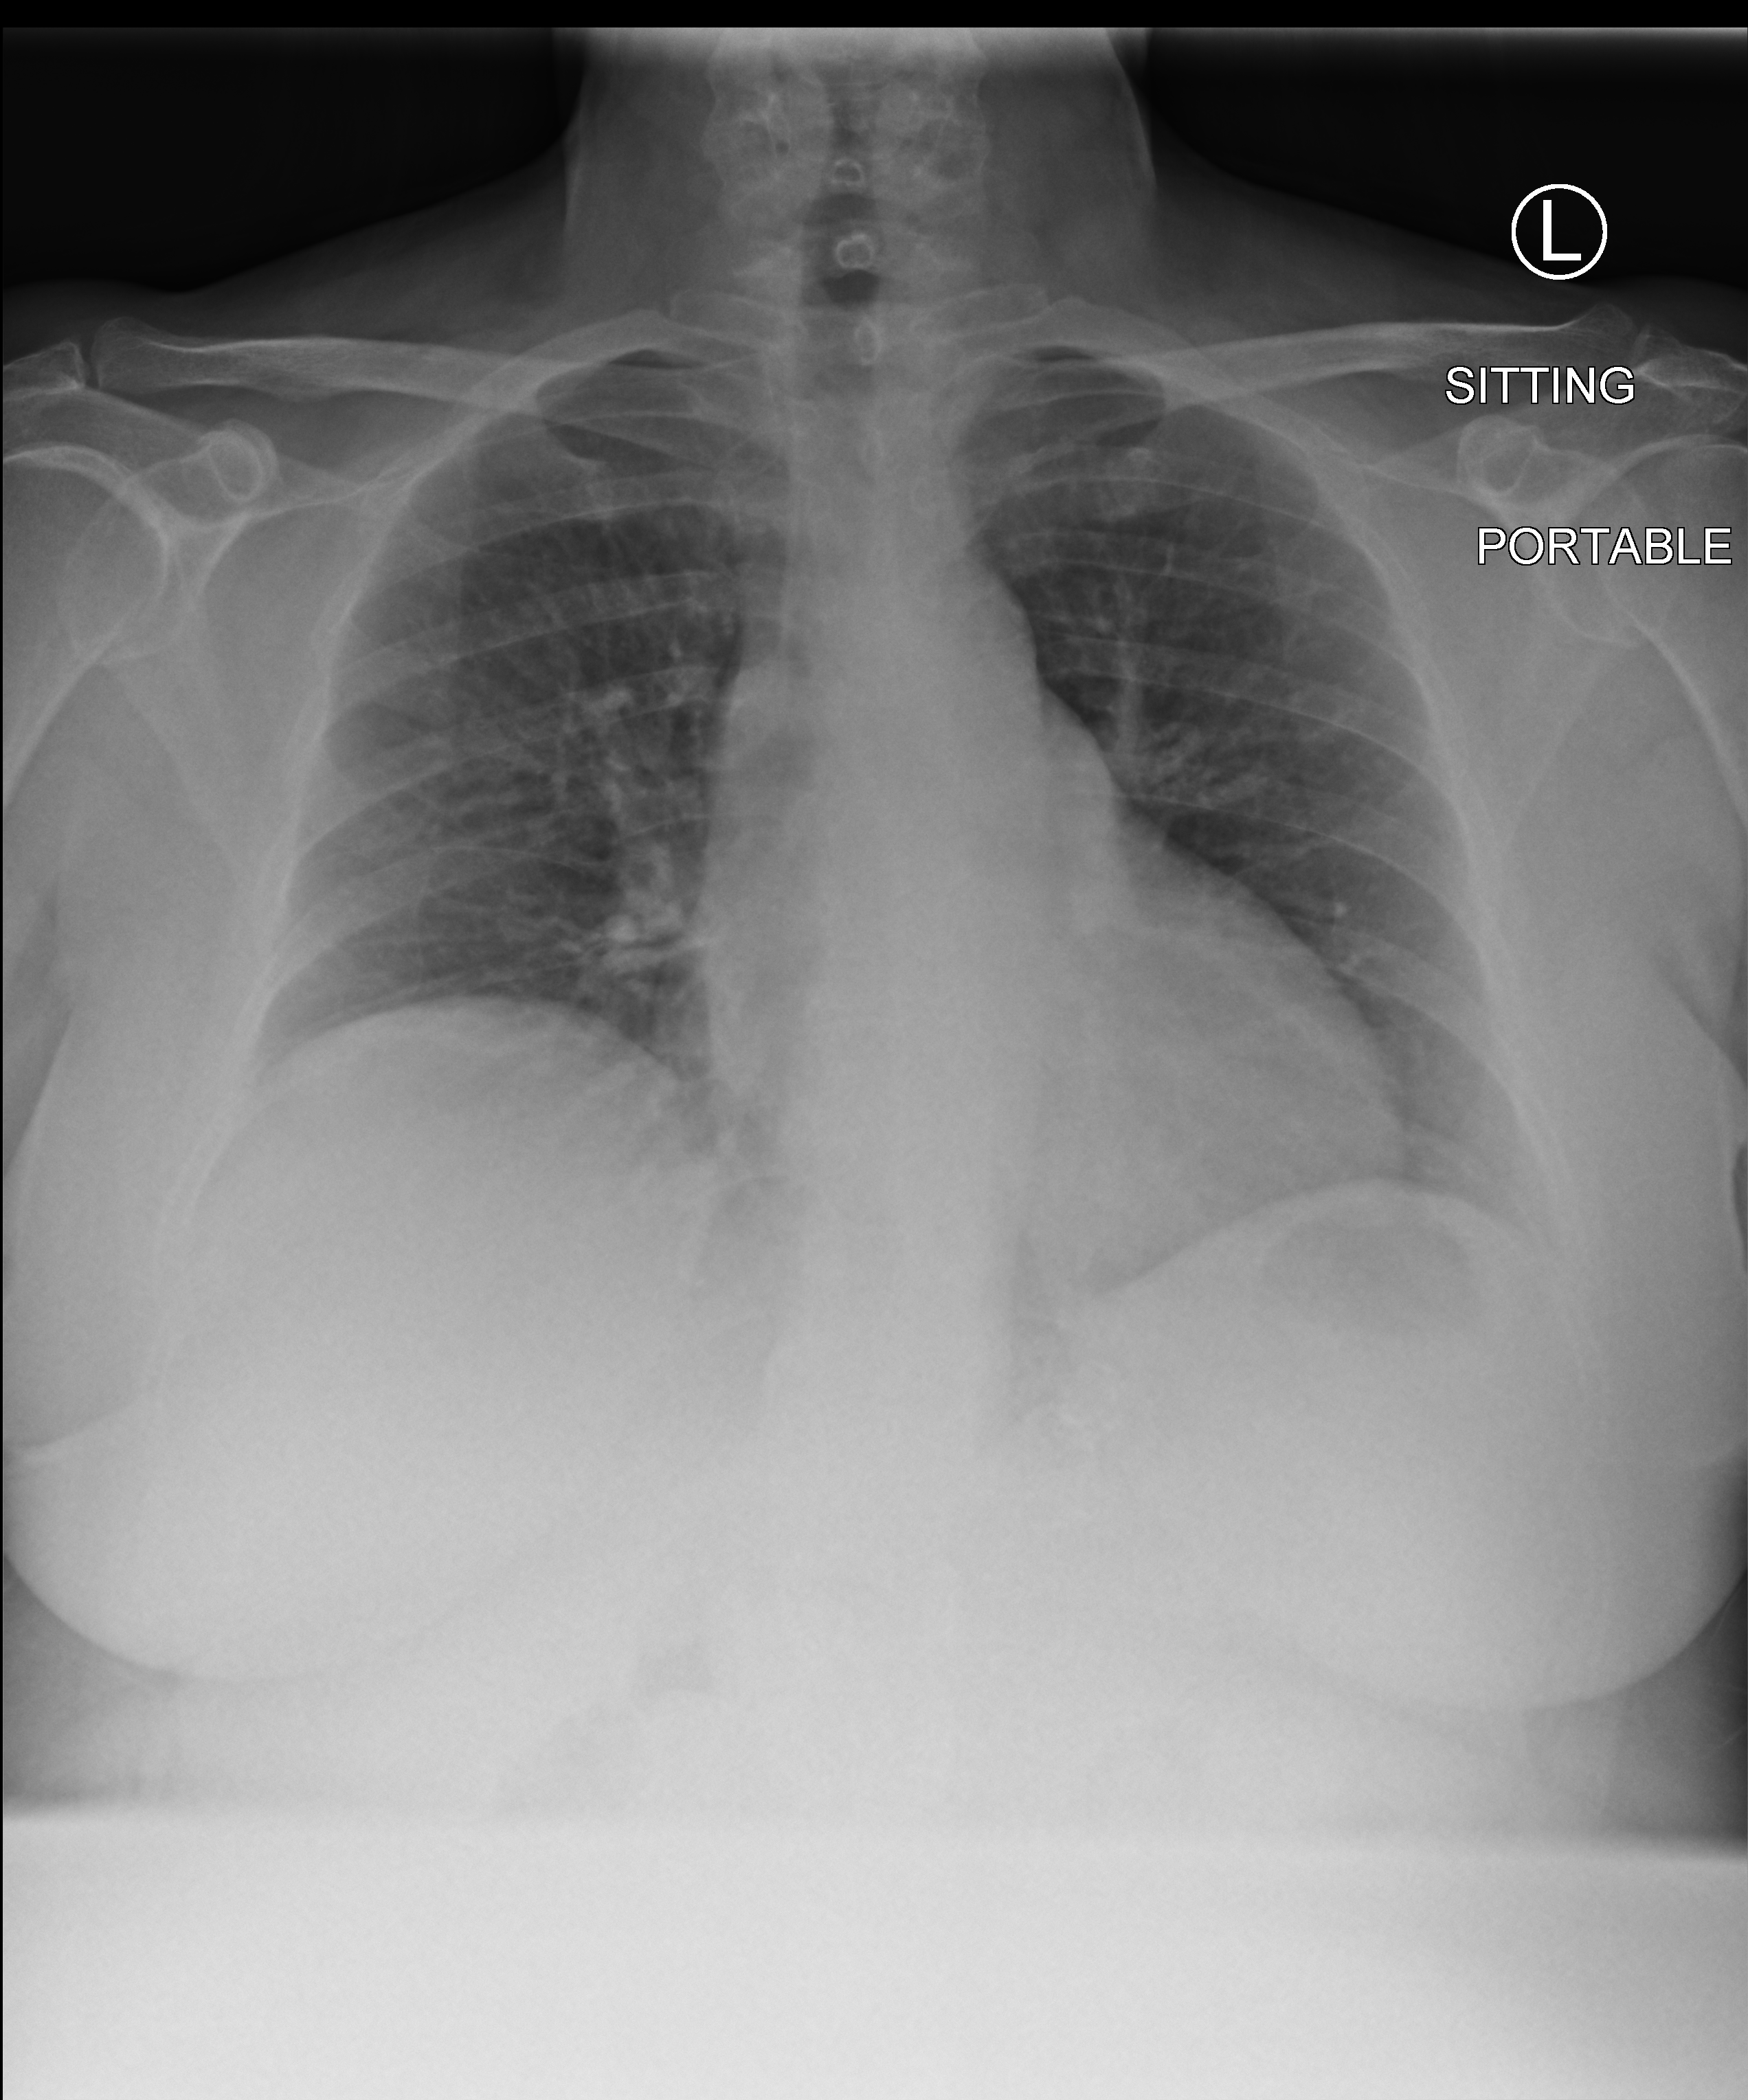
Bedside chest radiograph (computed radiography), anteroposterior (AP) projection. Female patient hospitalised with COVID-19, age 18–59 years.
From the hospital-stay record, not from the radiograph (when in the stay this image was taken is not recorded):
- chronic kidney disease (admission record): no